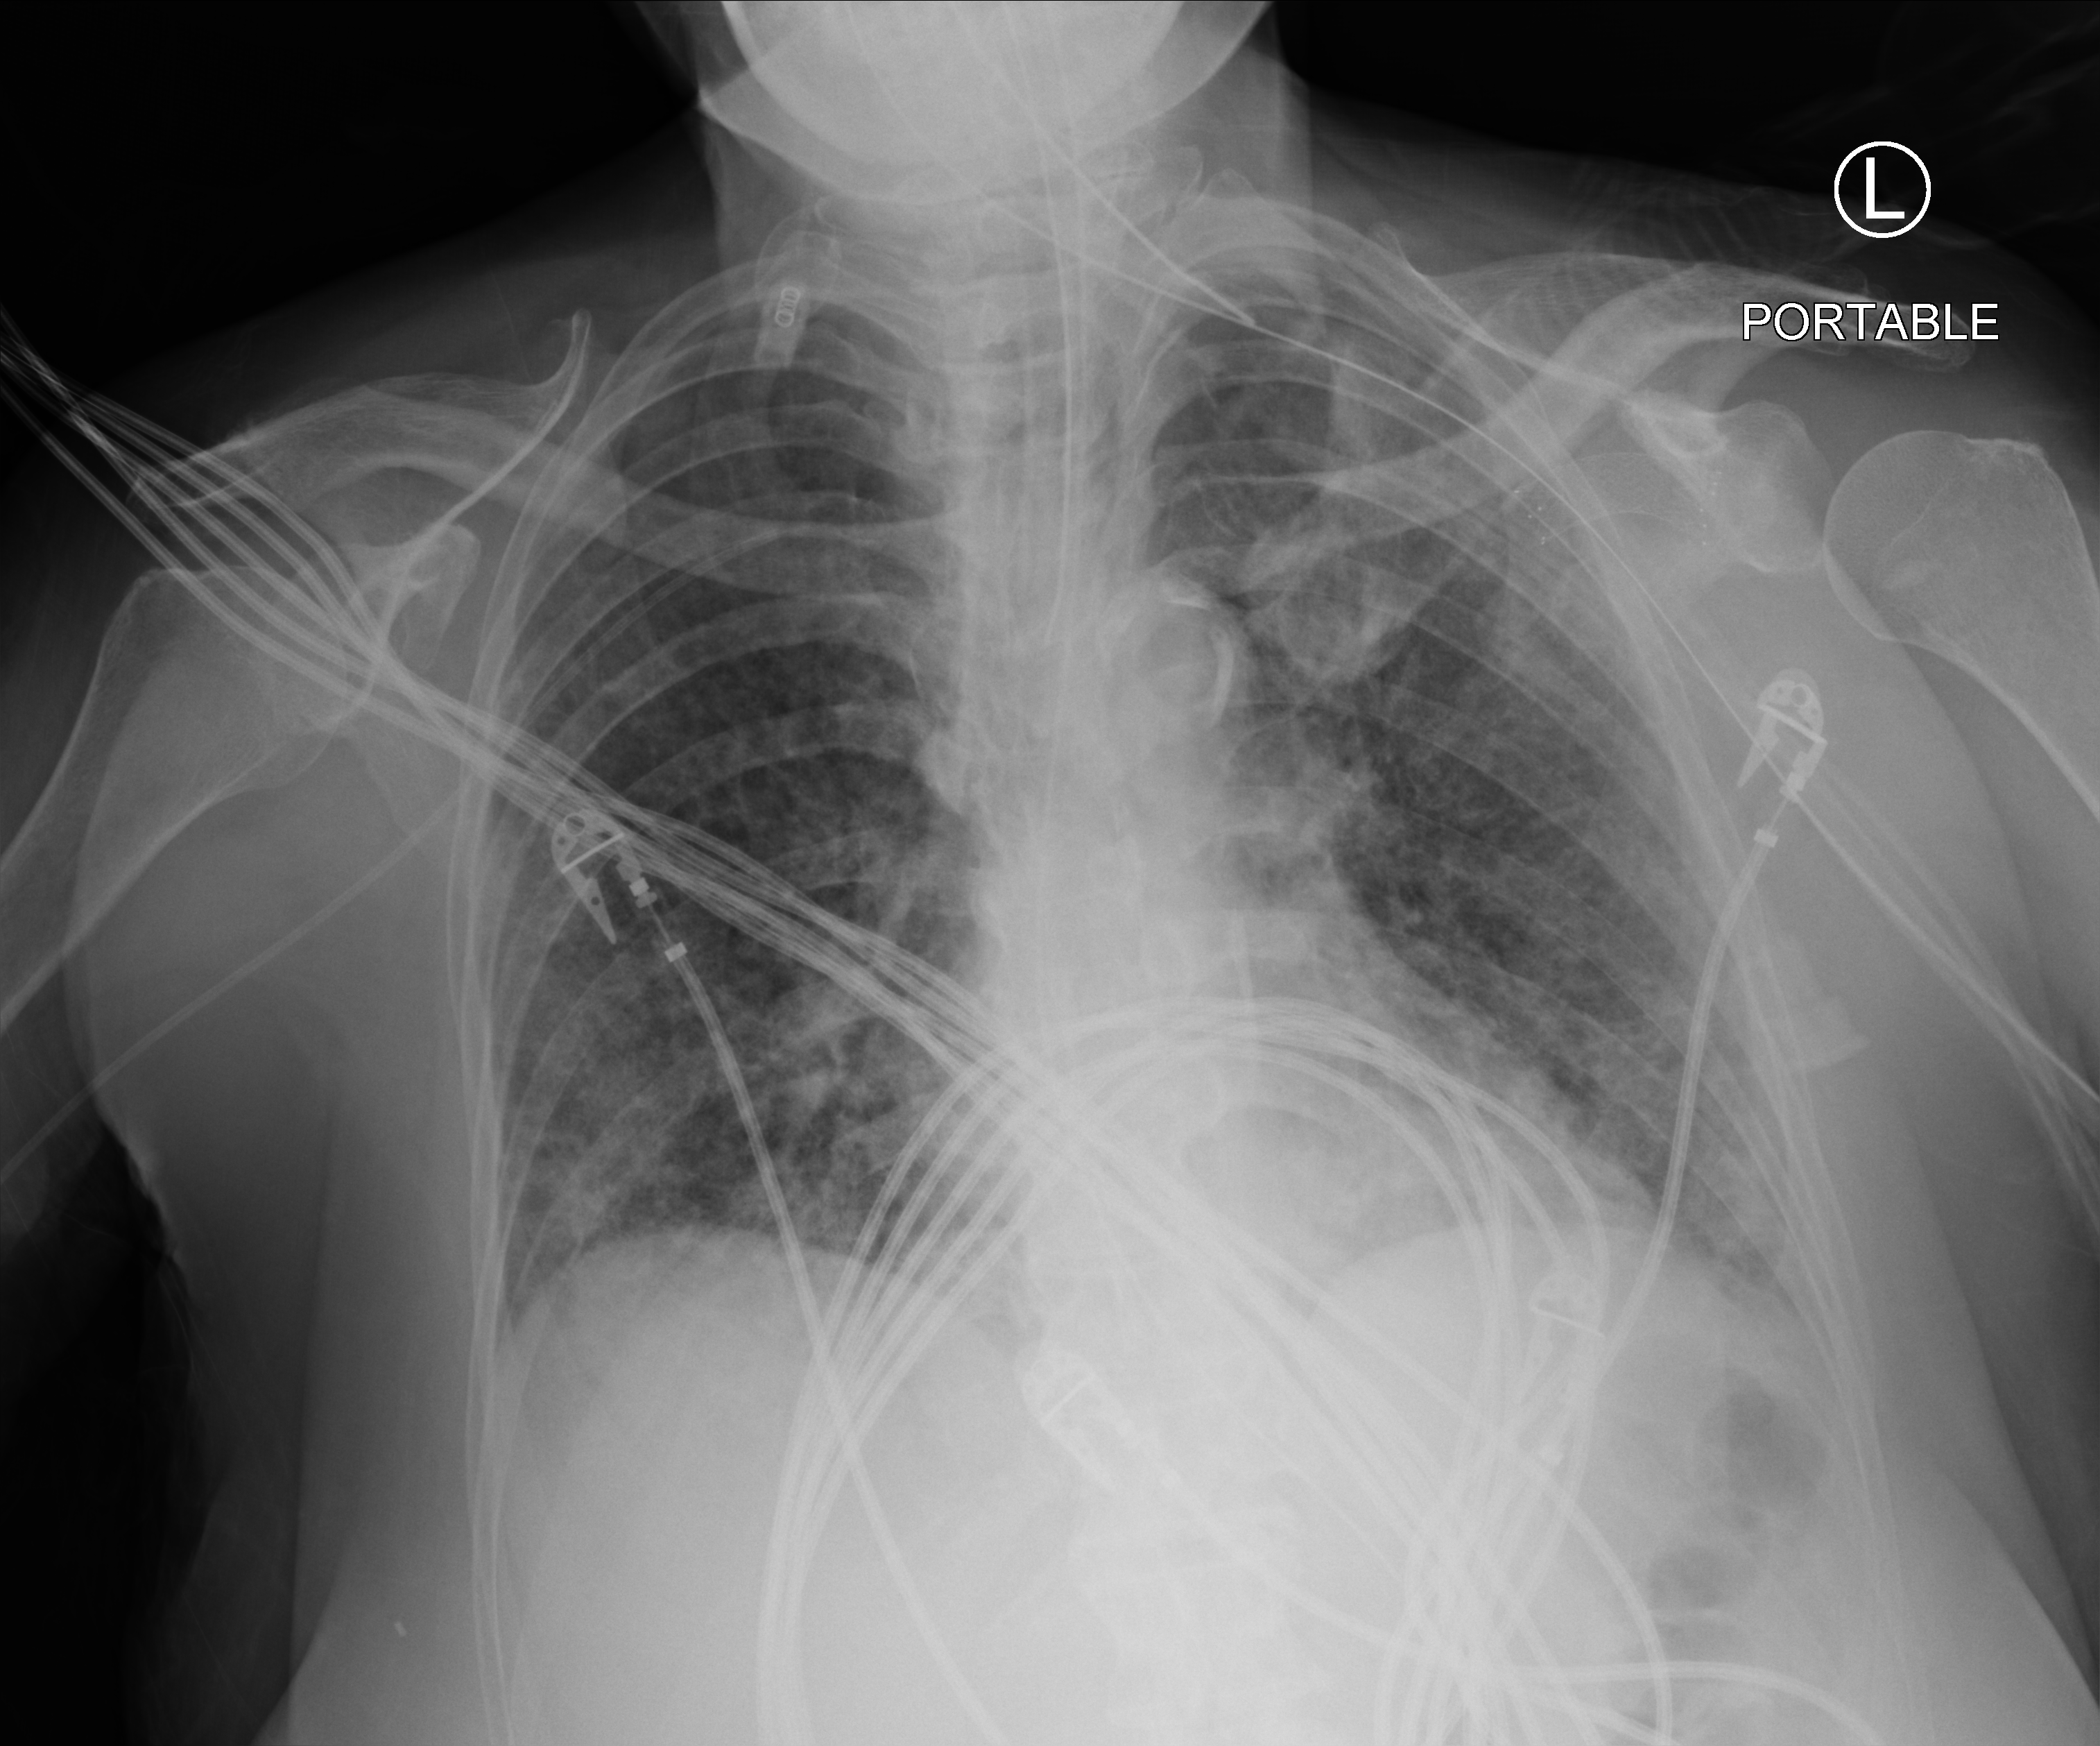
Chest X-ray (portable). Patient hospitalised with COVID-19; female, aged 60–74 years.
From the hospital-stay record, not from the radiograph (when in the stay this image was taken is not recorded): mechanically ventilated during this hospital stay: yes.